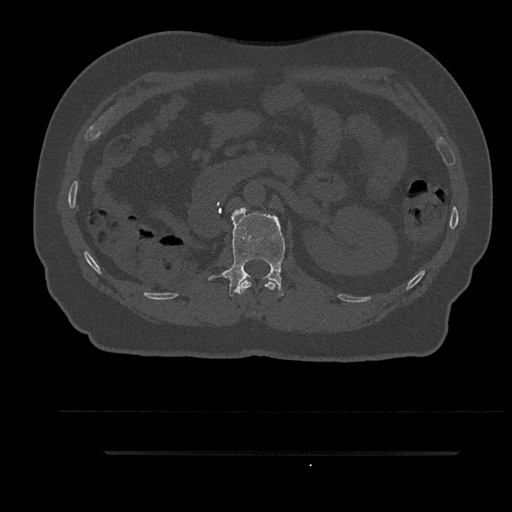
CT including the spine, one axial slice. Position 187 of 797 along the scan axis. Reconstruction kernel Br40s/3. 120 kVp. Bone window (W 1800 / L 400 HU). 0.5 mm slice thickness. 512 × 512 image matrix, field of view 432 × 432 mm. Patient: male, 63 years. From the clinical record (not read from this slice): primary cancer: renal; vertebrae with lytic lesions (as recorded): T8.
Outlined on this slice (semi-automatically segmented with operator editing):
- L1 vertebra: bounding box (x1, y1, x2, y2) in pixels: (209, 208, 285, 297)
- T12 vertebra: (240, 280, 277, 293)